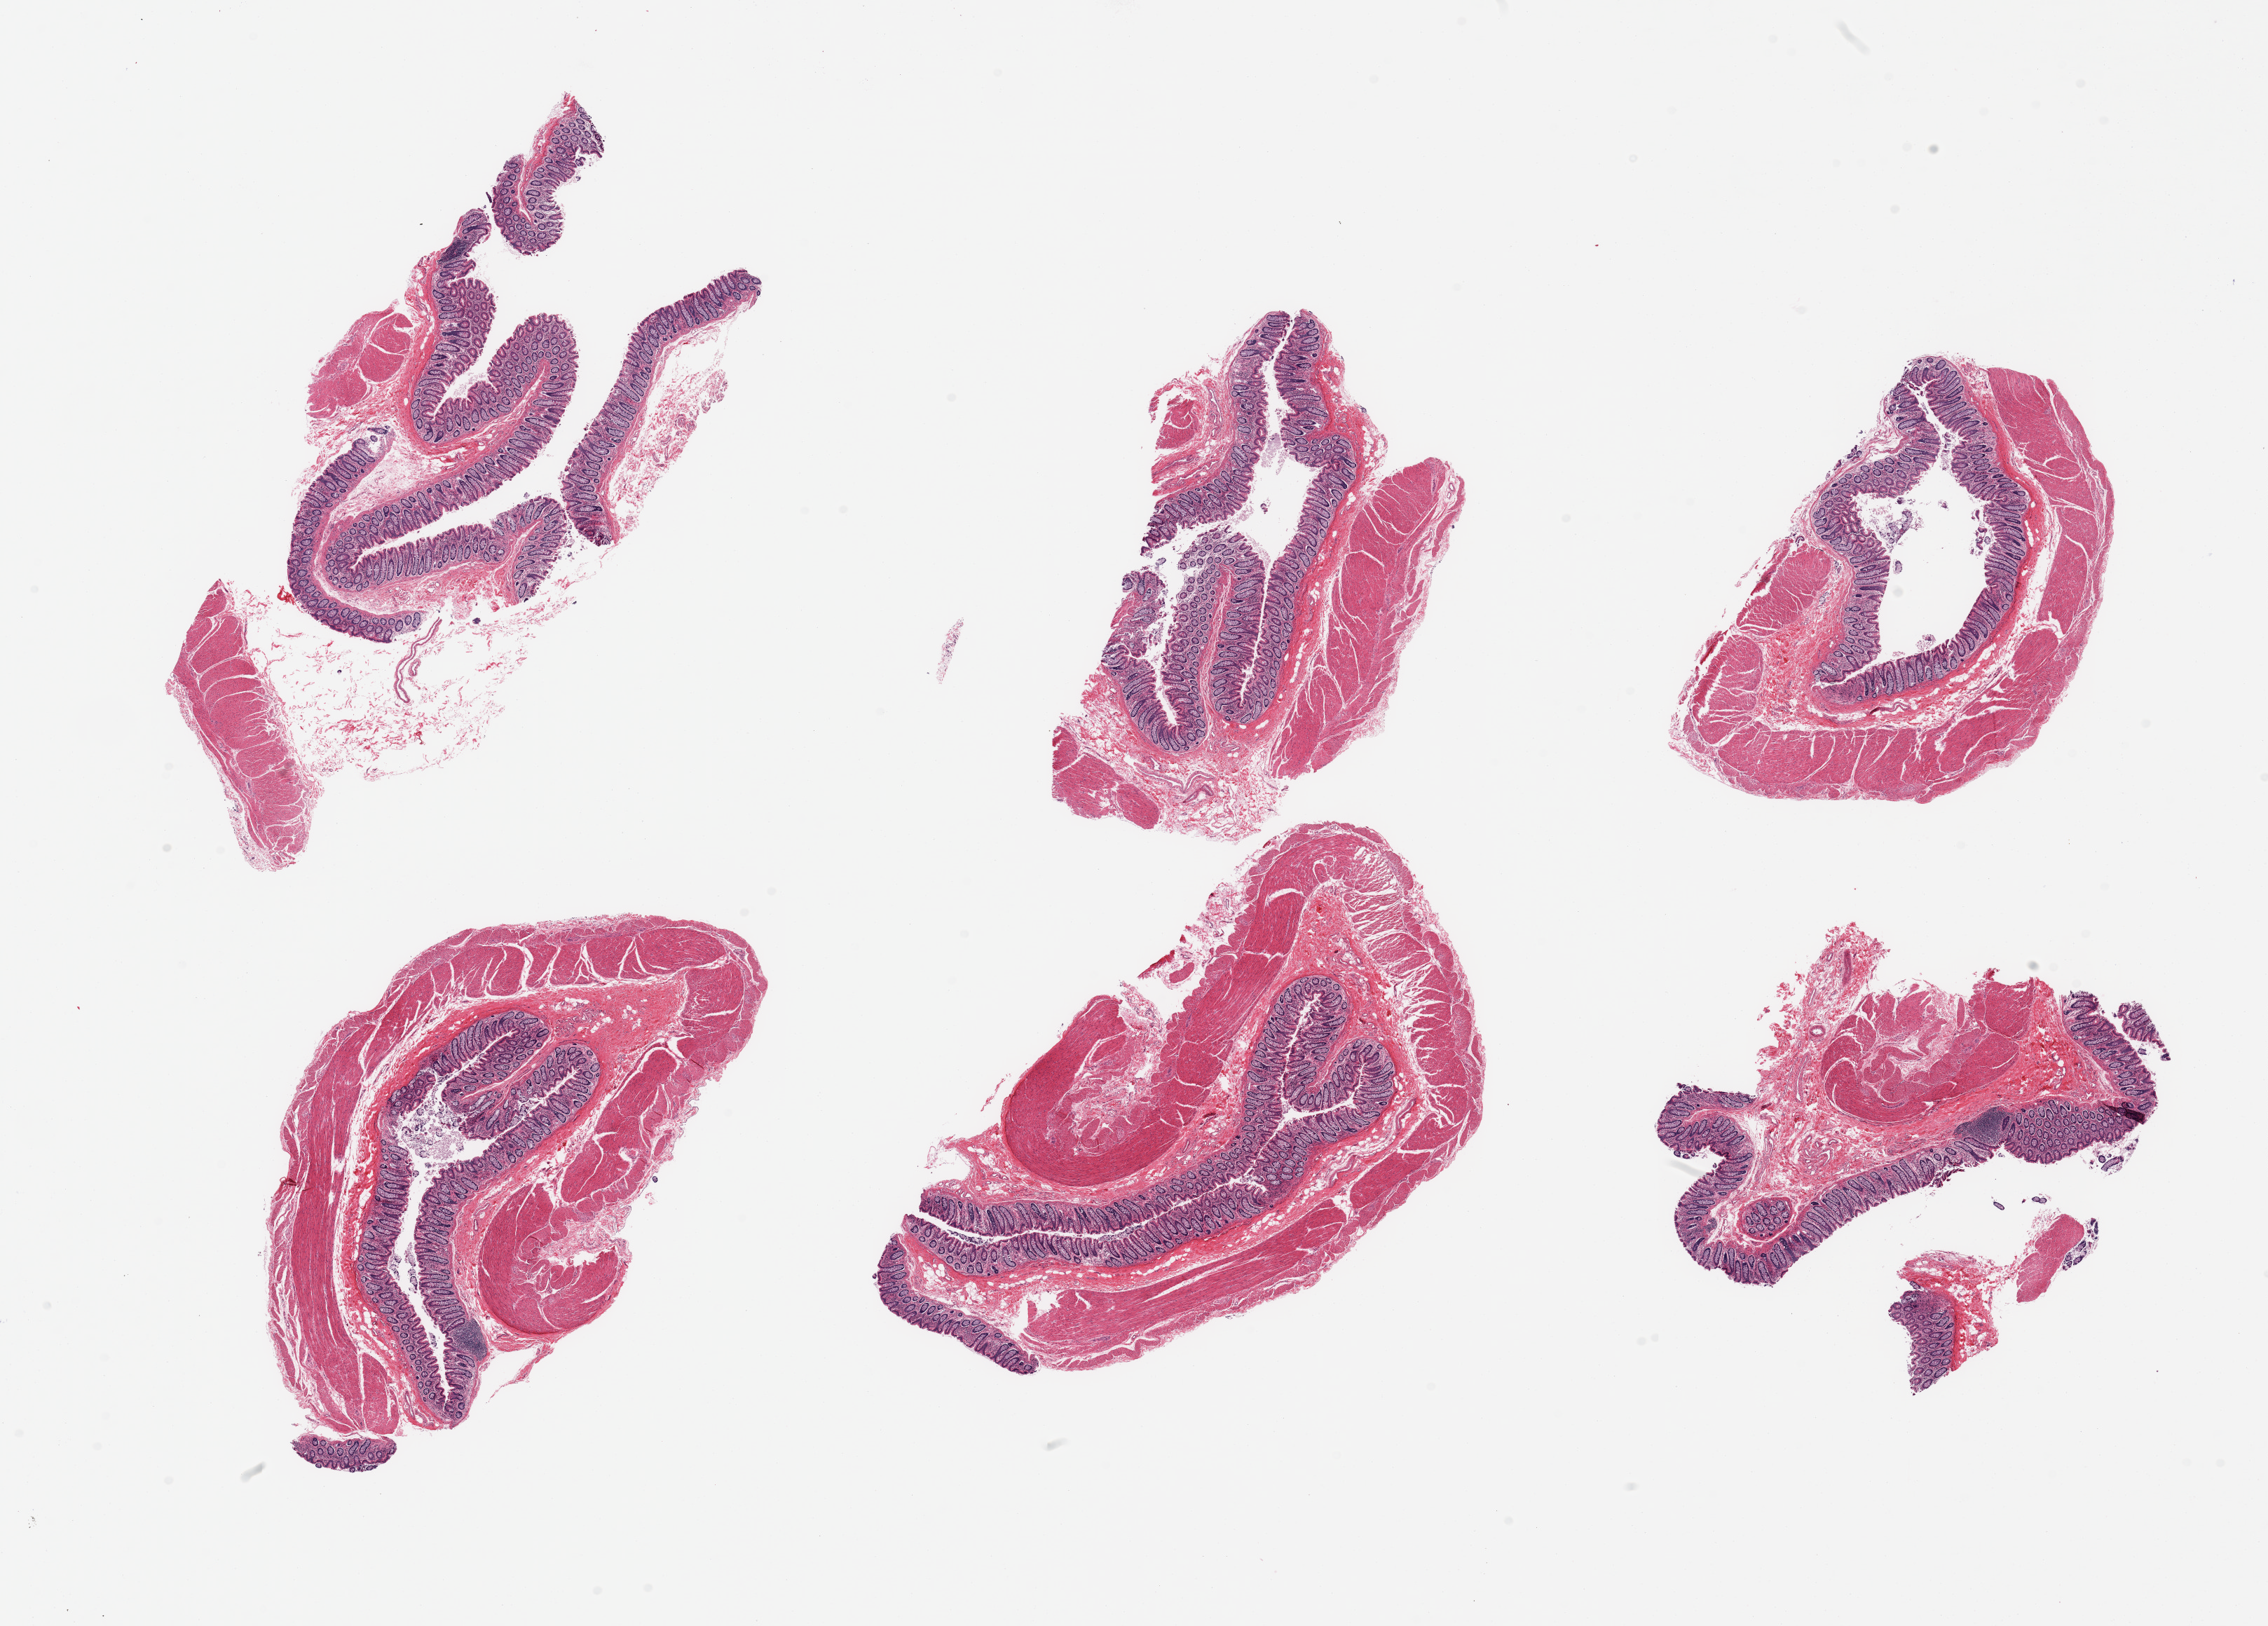
Digitized haematoxylin and eosin-stained section, brightfield, low-resolution overview of the scanned area, about 25.6 x 18.4 mm, PAXgene-fixed, paraffin-embedded tissue, sampled site (target tissue): transverse colon, donor tissue sample. Female donor.
- reviewer comment on this tissue sample: 6 pieces; full thickness sections of colon